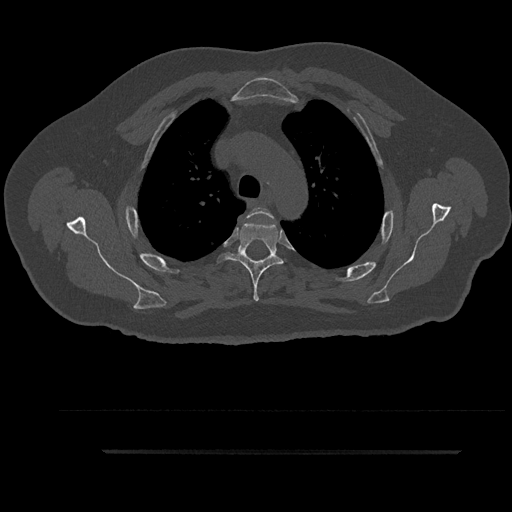
CT including the spine, one axial slice; slice 676 of 797 in the series (ordered by position); reconstruction kernel Br40s/3; bone window (W 1800 / L 400 HU); 0.5 mm slice thickness; 512 × 512 image matrix, field of view 432 × 432 mm. Male patient, age 63 years. From the clinical record (not read from this slice): primary cancer: renal; vertebrae with lytic lesions (as recorded): T8.
Annotated regions visible in this slice (semi-automatically segmented with operator editing):
- T3 vertebra: bounding box [x1, y1, x2, y2] px = [247, 207, 275, 259]
- T4 vertebra: [217, 221, 284, 301]